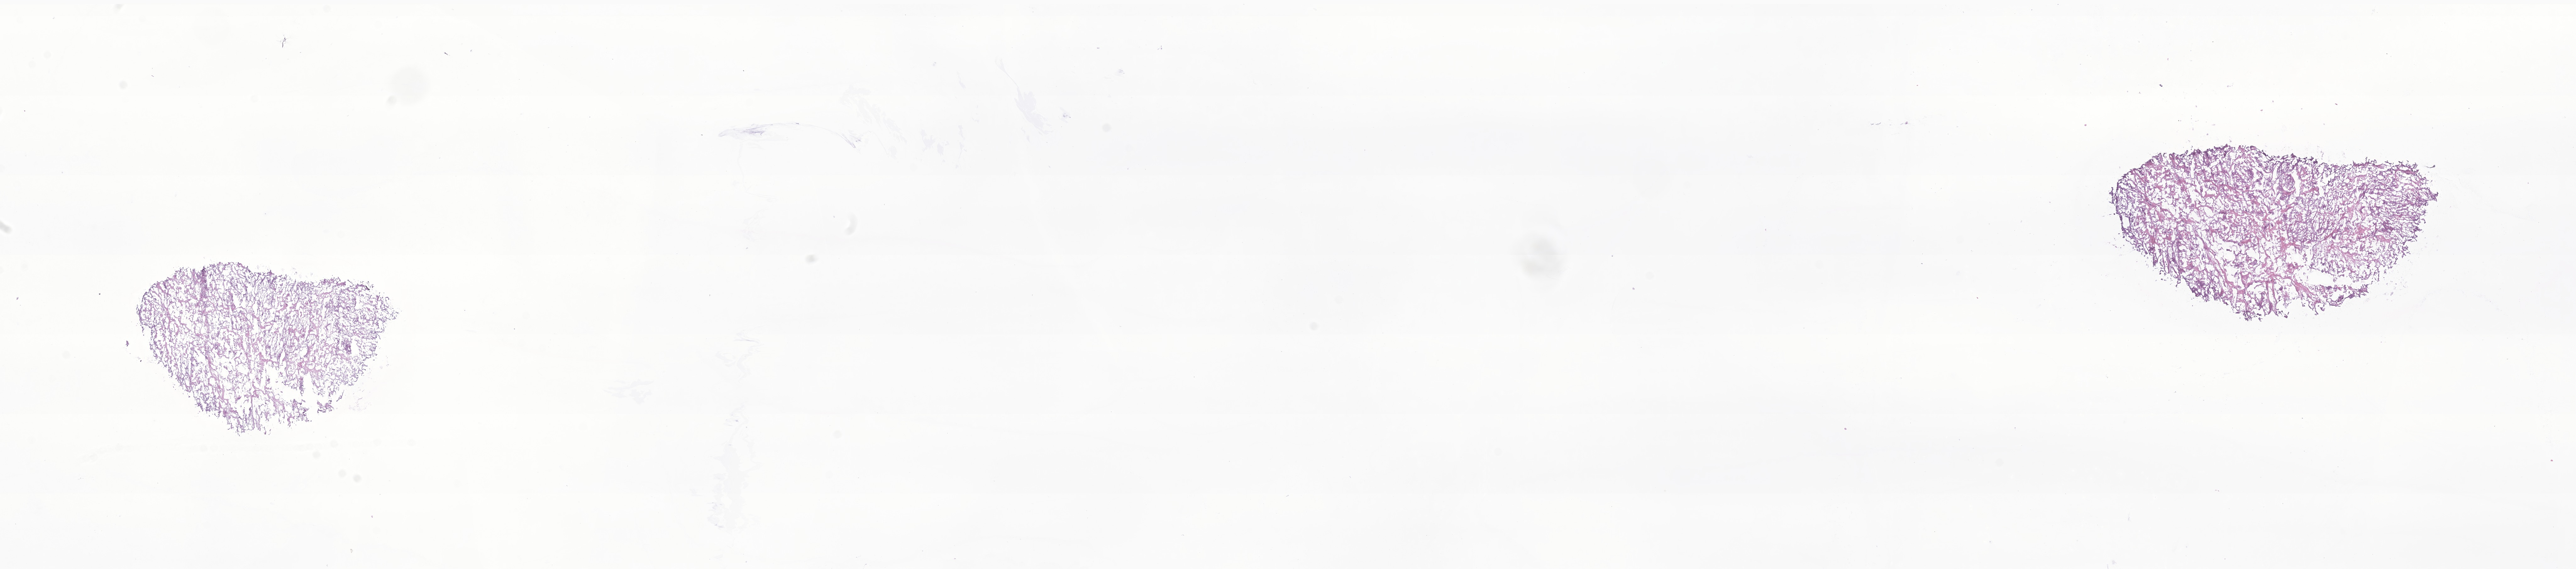
Whole-slide image, hematoxylin and eosin (H&E) stain of tumor tissue from the brain, shown as a low-resolution overview of the whole scanned area (about 34.5 x 7.6 mm); frozen section. Patient: female, age 37 months.
- recorded diagnosis: Clear cell meningioma